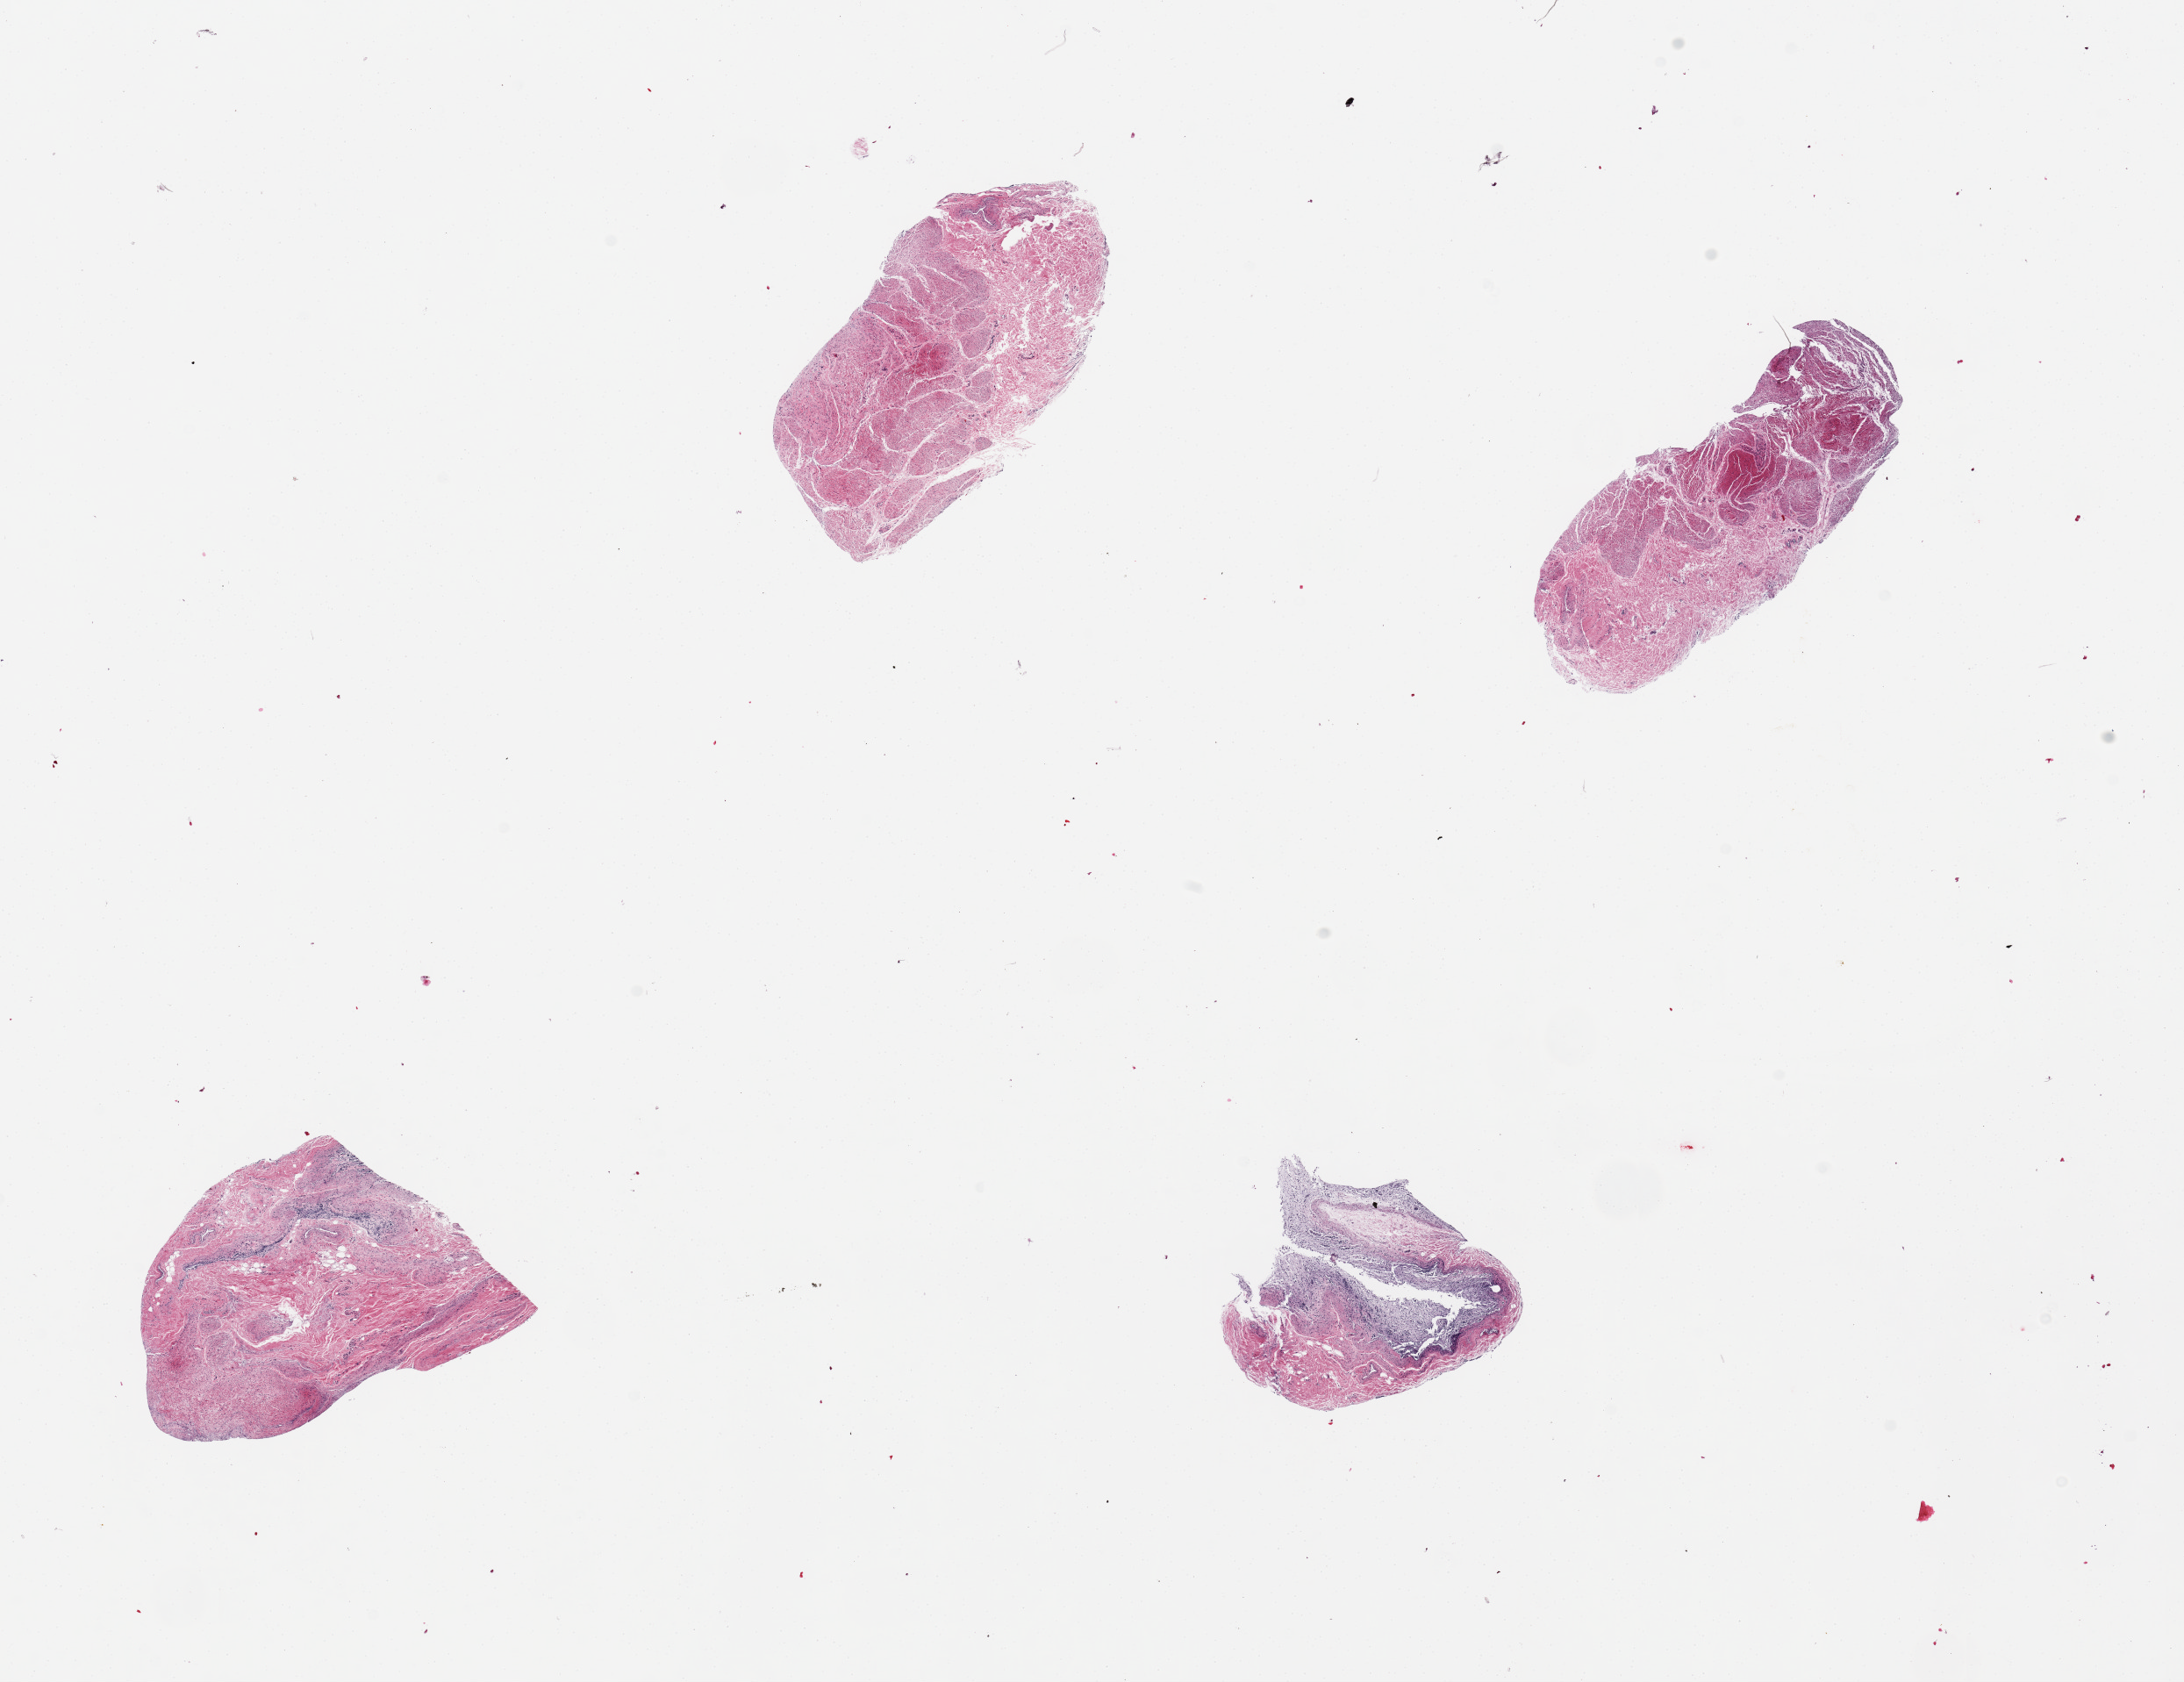
Digitized hematoxylin and eosin (H&E)-stained section, a low-resolution overview of the entire scanned area, about 19.7 x 15.2 mm (acquisition: 20x scan). PAXgene-fixed paraffin-embedded (PFPE) section. Target tissue: stomach. Tissue donor sample. Donor: male.
- reviewer comment on this tissue sample: 4 pieces. Mucosa largely sloughed; where present, badly autolyzed, no visible landmarks